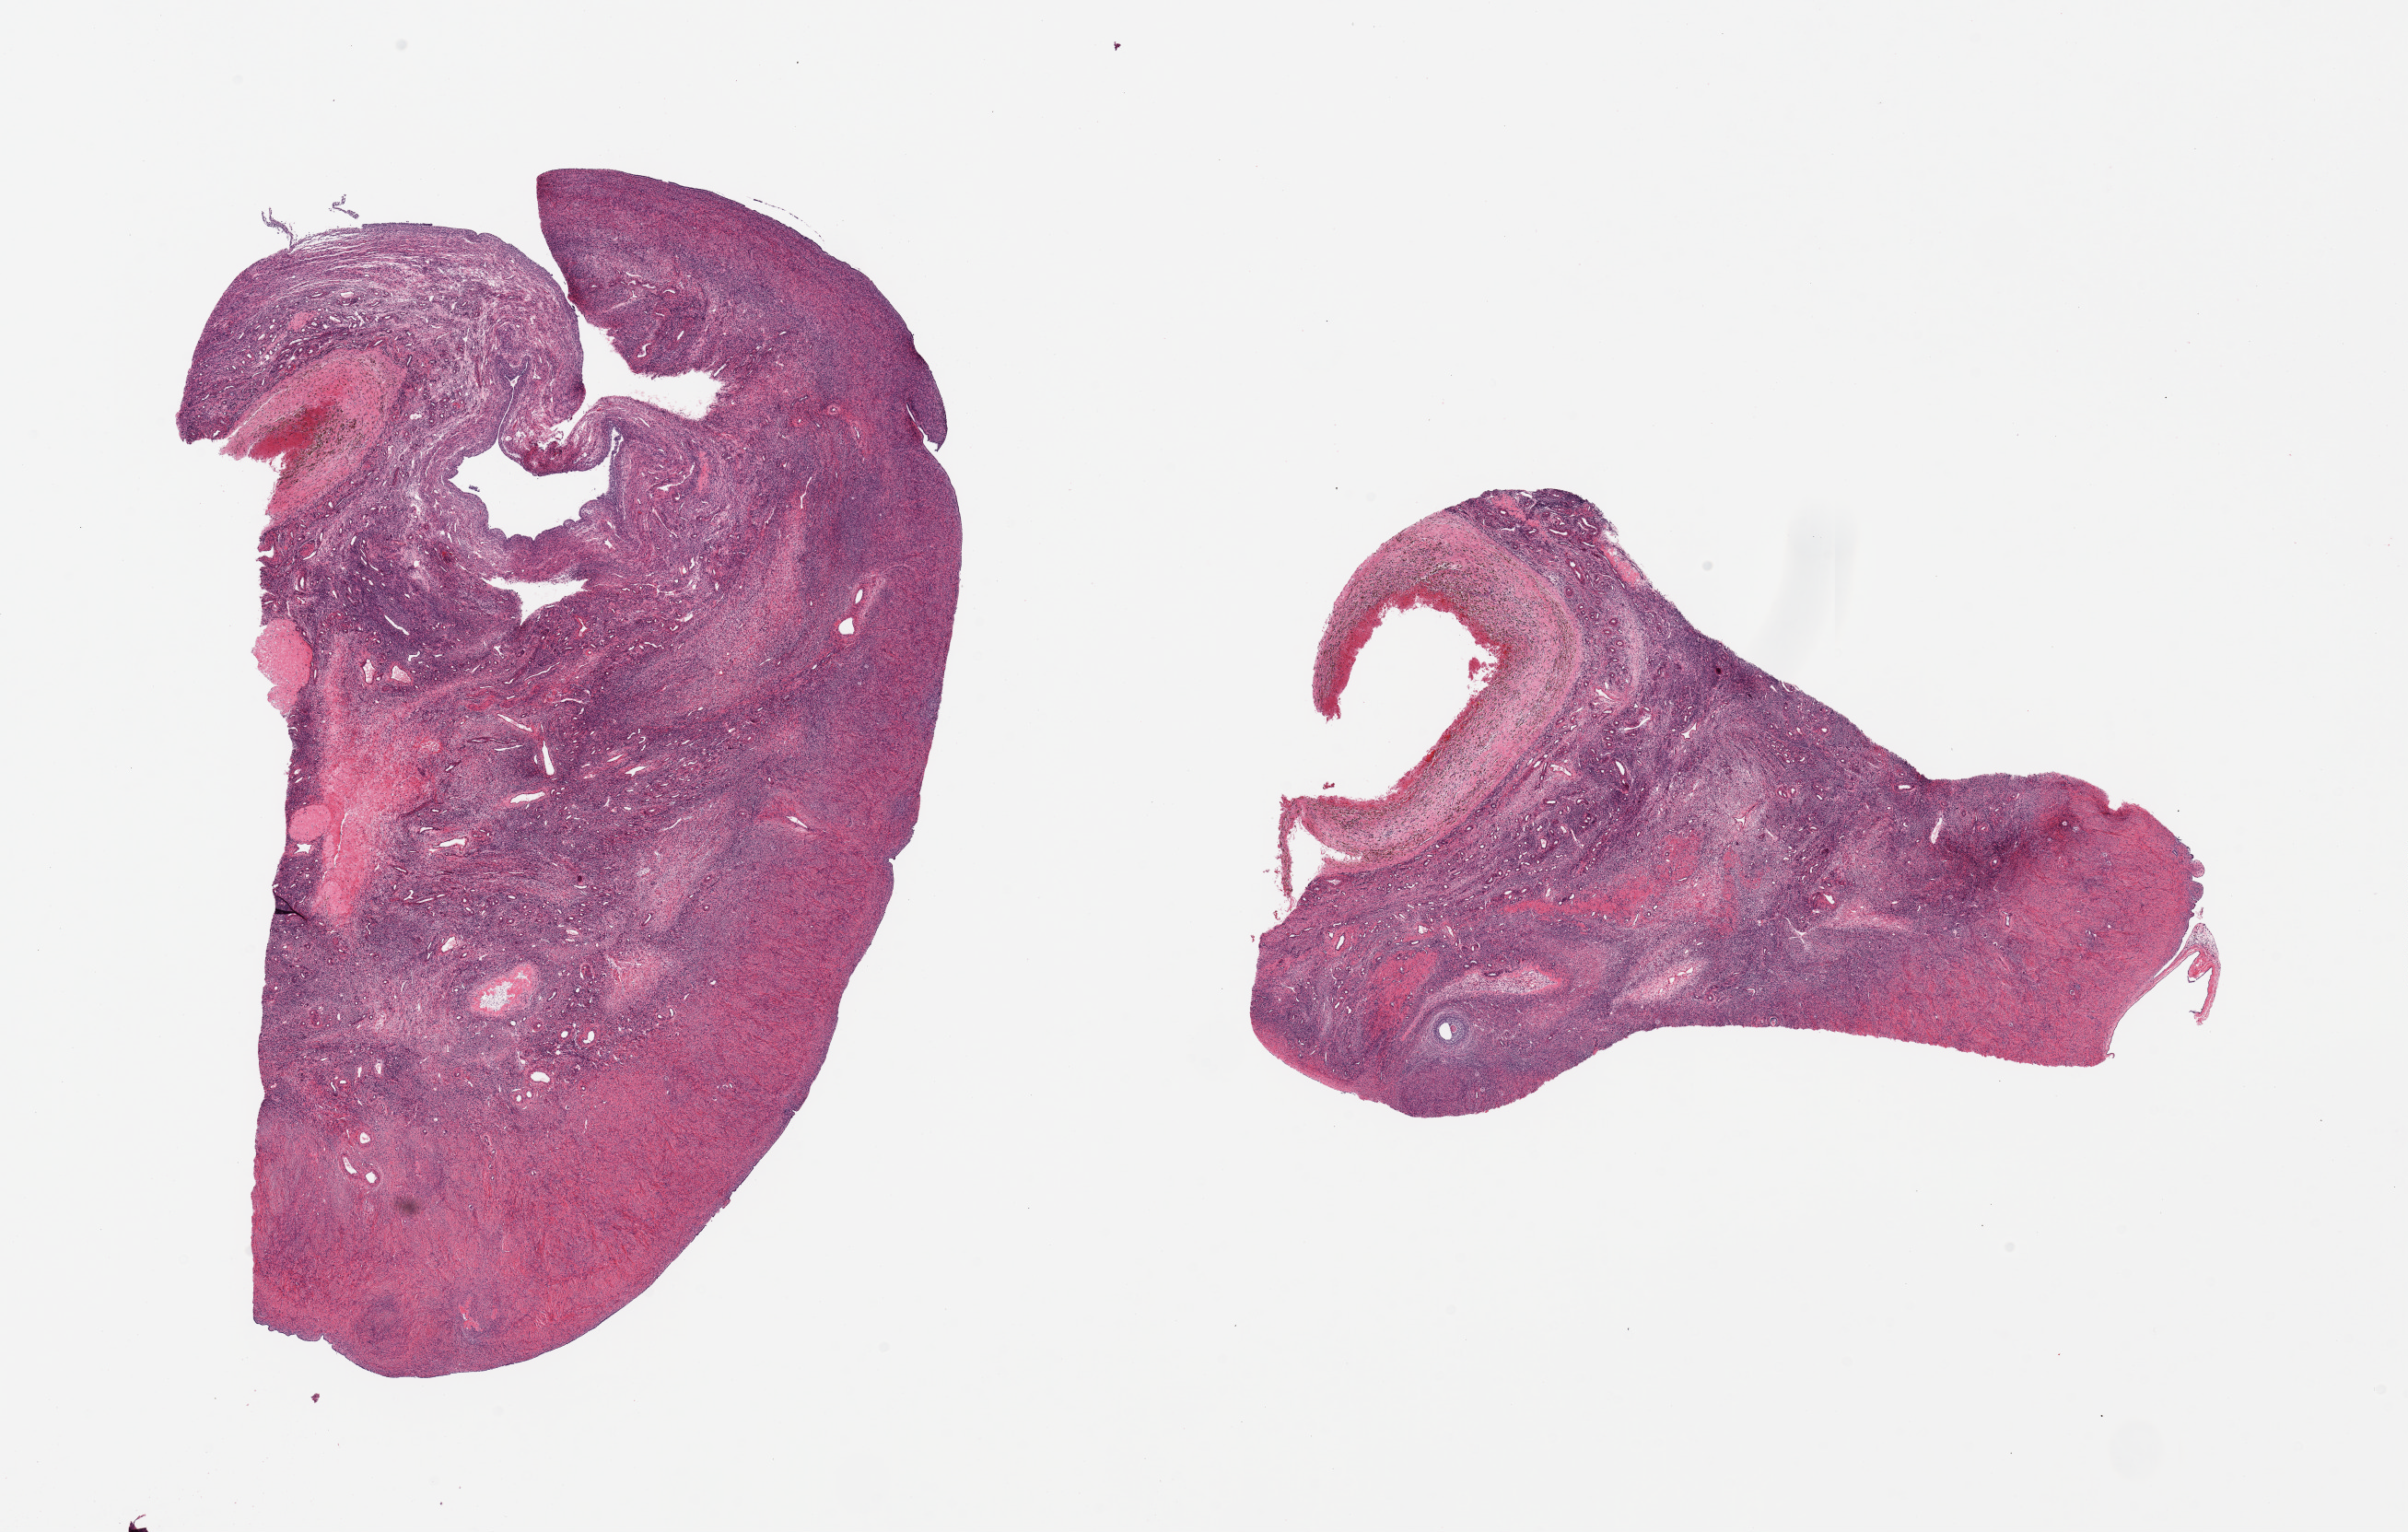
Digitized haematoxylin and eosin-stained section — whole scanned area (about 20.7 x 13.2 mm) shown as a low-resolution overview; PAXgene-fixed paraffin-embedded (PFPE) section; section of ovary (target tissue); tissue donor sample.
Review note (as recorded): 2 pieces.